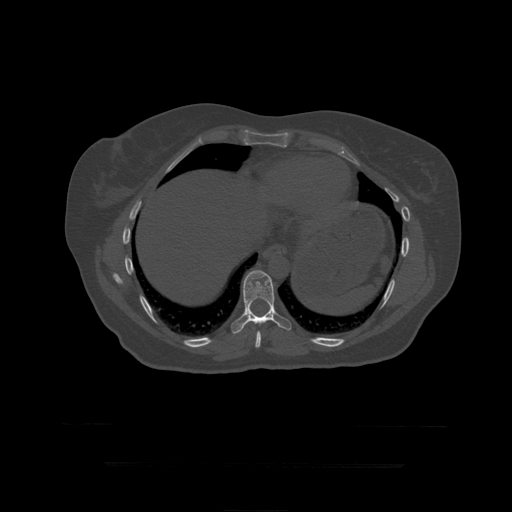
CT including the spine, one axial slice. Slice 245 of 399 in the series (ordered by position). Reconstruction kernel STANDARD. Bone window (W 1800 / L 400 HU). 1.25 mm slice thickness. 512 × 512 image matrix. Patient age 41 years. From the clinical record (not read from this slice): primary cancer: breast.
Annotated regions visible in this slice (semi-automatic segmentation, software-assisted and operator-edited):
- T10 vertebra: bounding box <231,271,292,334> (left, top, right, bottom; pixels)
- T9 vertebra: <256,331,262,348>